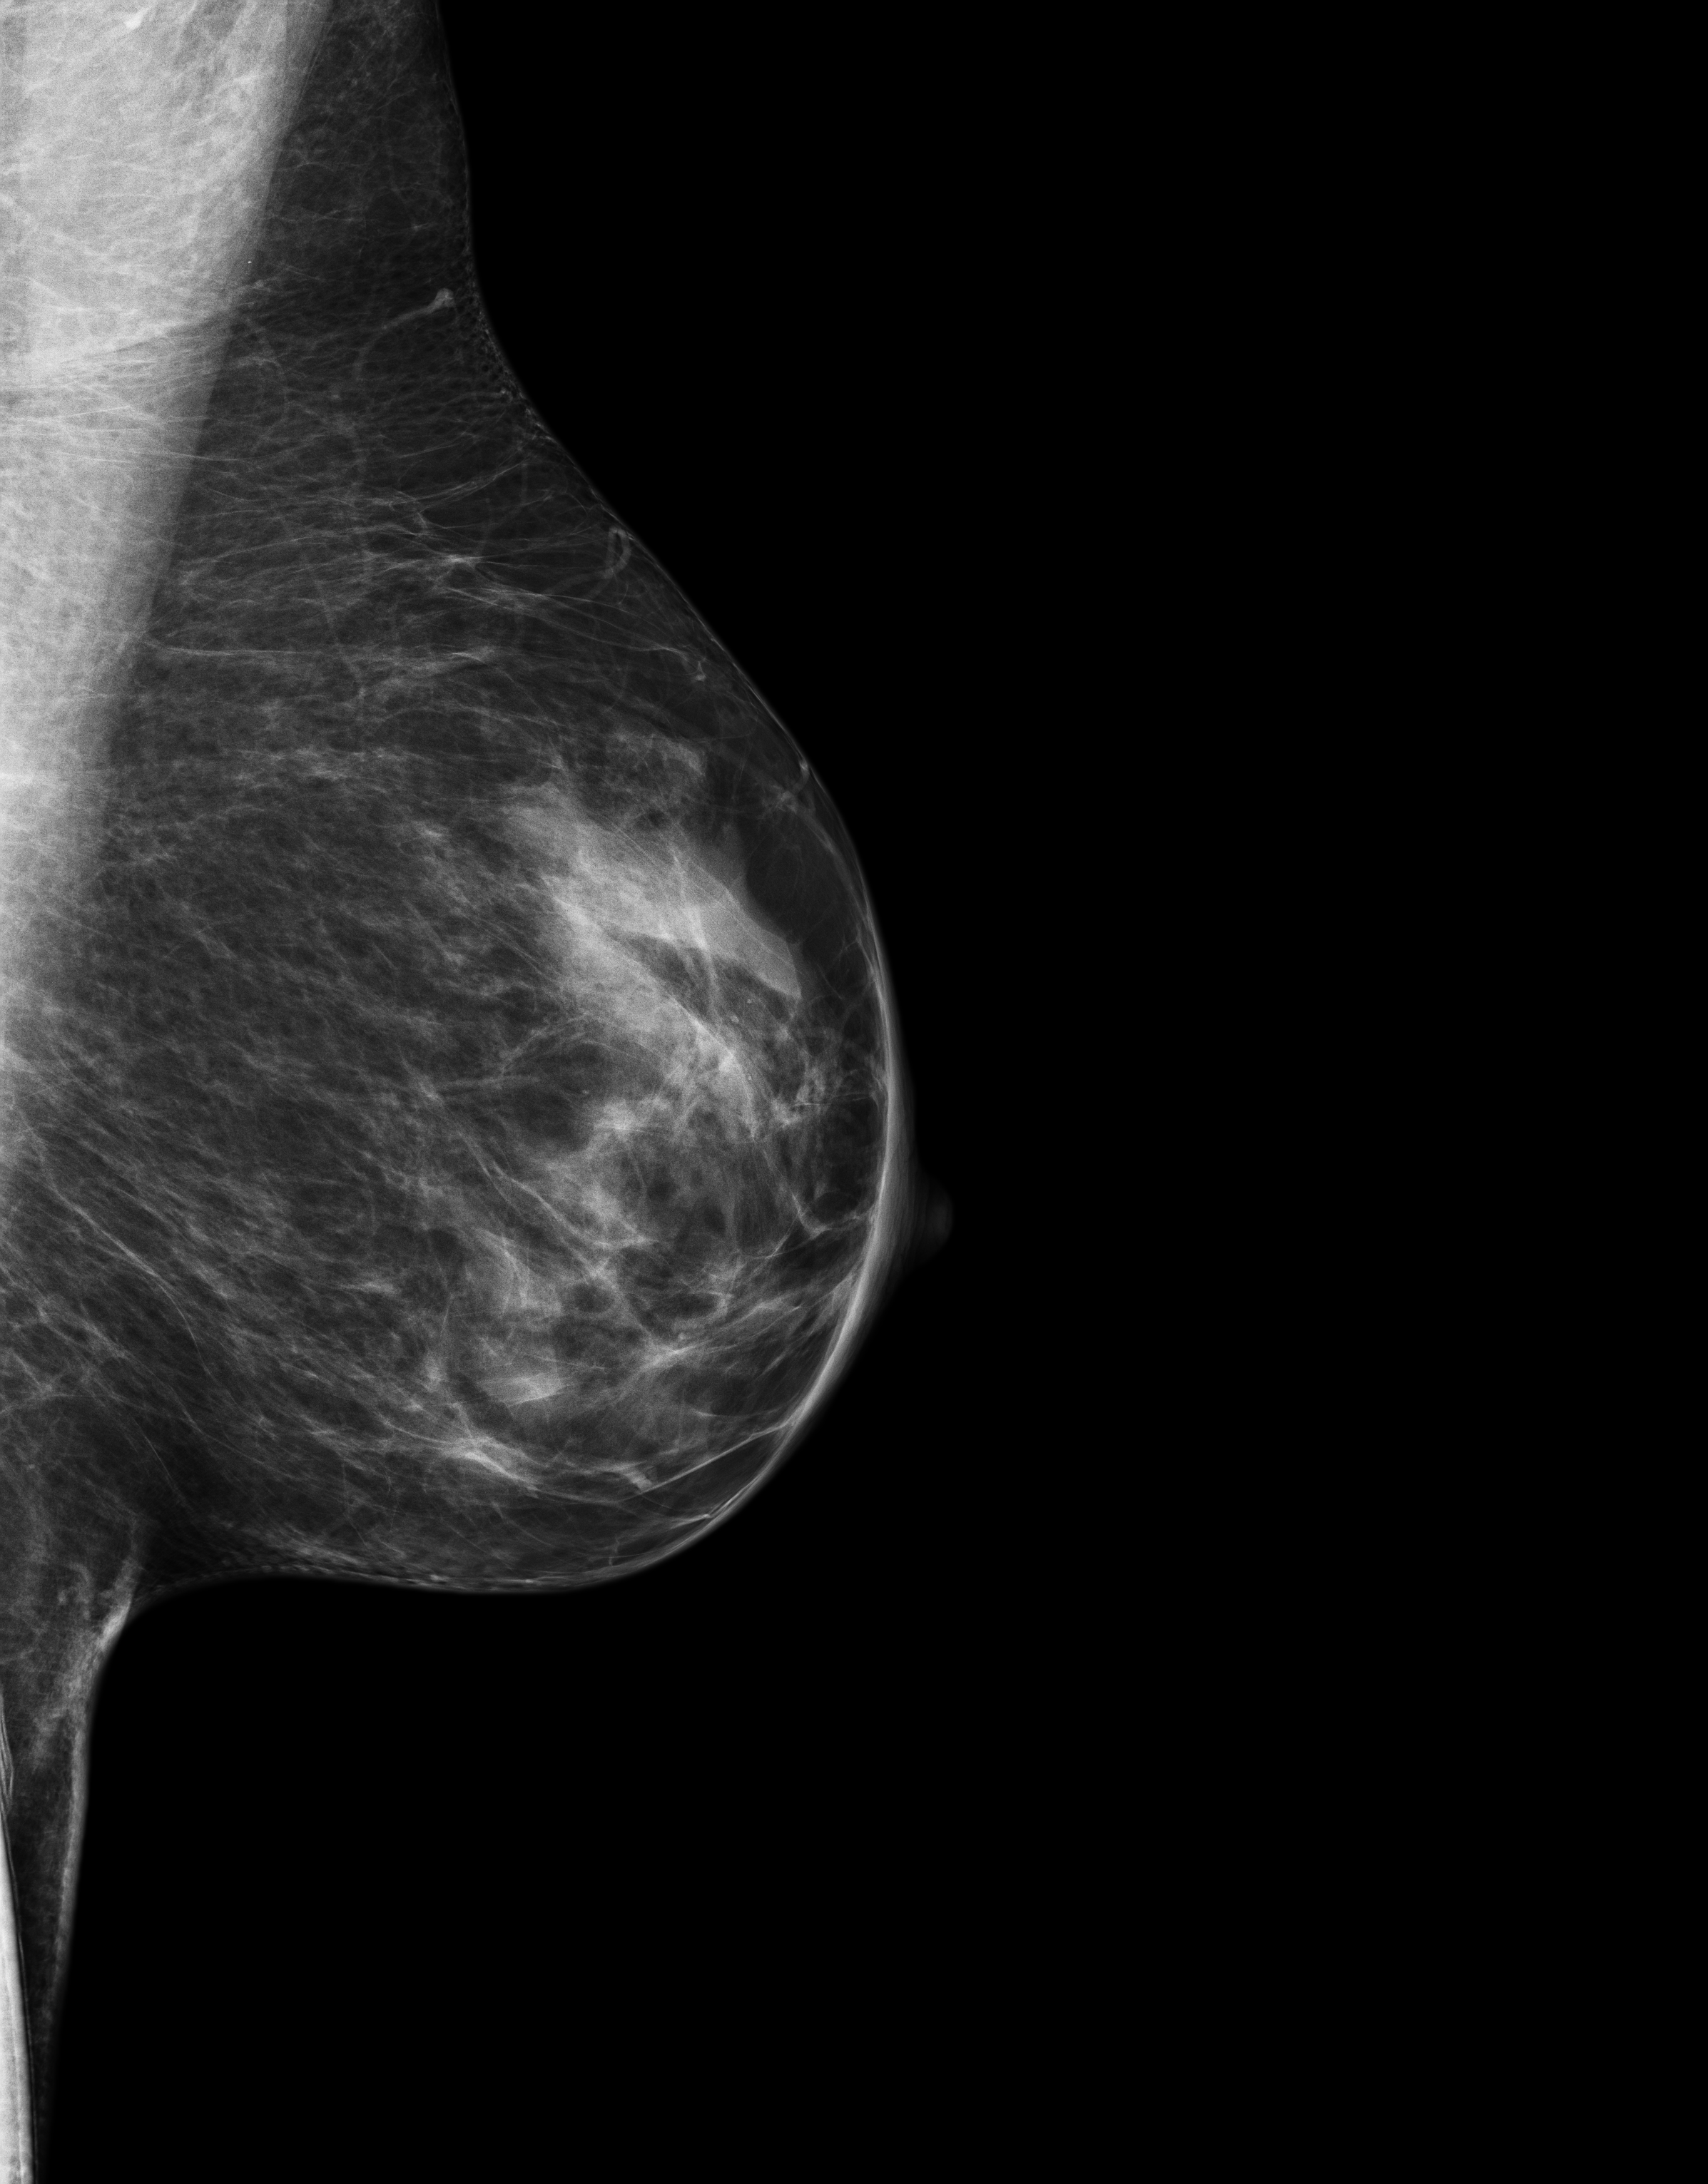
Full-field digital mammogram (FFDM); left breast; mediolateral oblique (MLO) view; annual screening mammography examination. Patient: female, 48 years.
BI-RADS breast density category at the screening exam (both breasts, scale 1–4): 3. Final BI-RADS assessment for this screening round (tomosynthesis exam, both breasts): category 2. Recall: no recall after this screen.